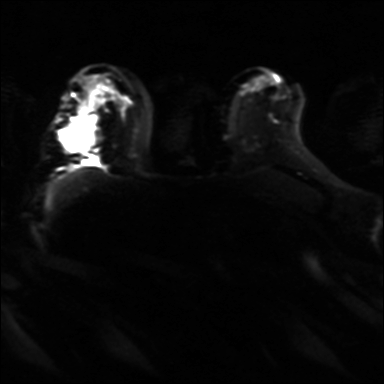
Breast MRI, one axial slice; slice 23 of 36 in the series (ordered by position); diffusion-weighted series; image 2 of 4 stored at this slice position (different b-values; order by instance number); 3 T; 4 mm slice thickness; 384 × 384 image matrix, field of view 320 × 320 mm. Female patient.
Structures marked on this image (expert manual segmentation):
- tumour on diffusion-weighted imaging: bounding box [x1, y1, x2, y2] px = [60, 115, 97, 152]